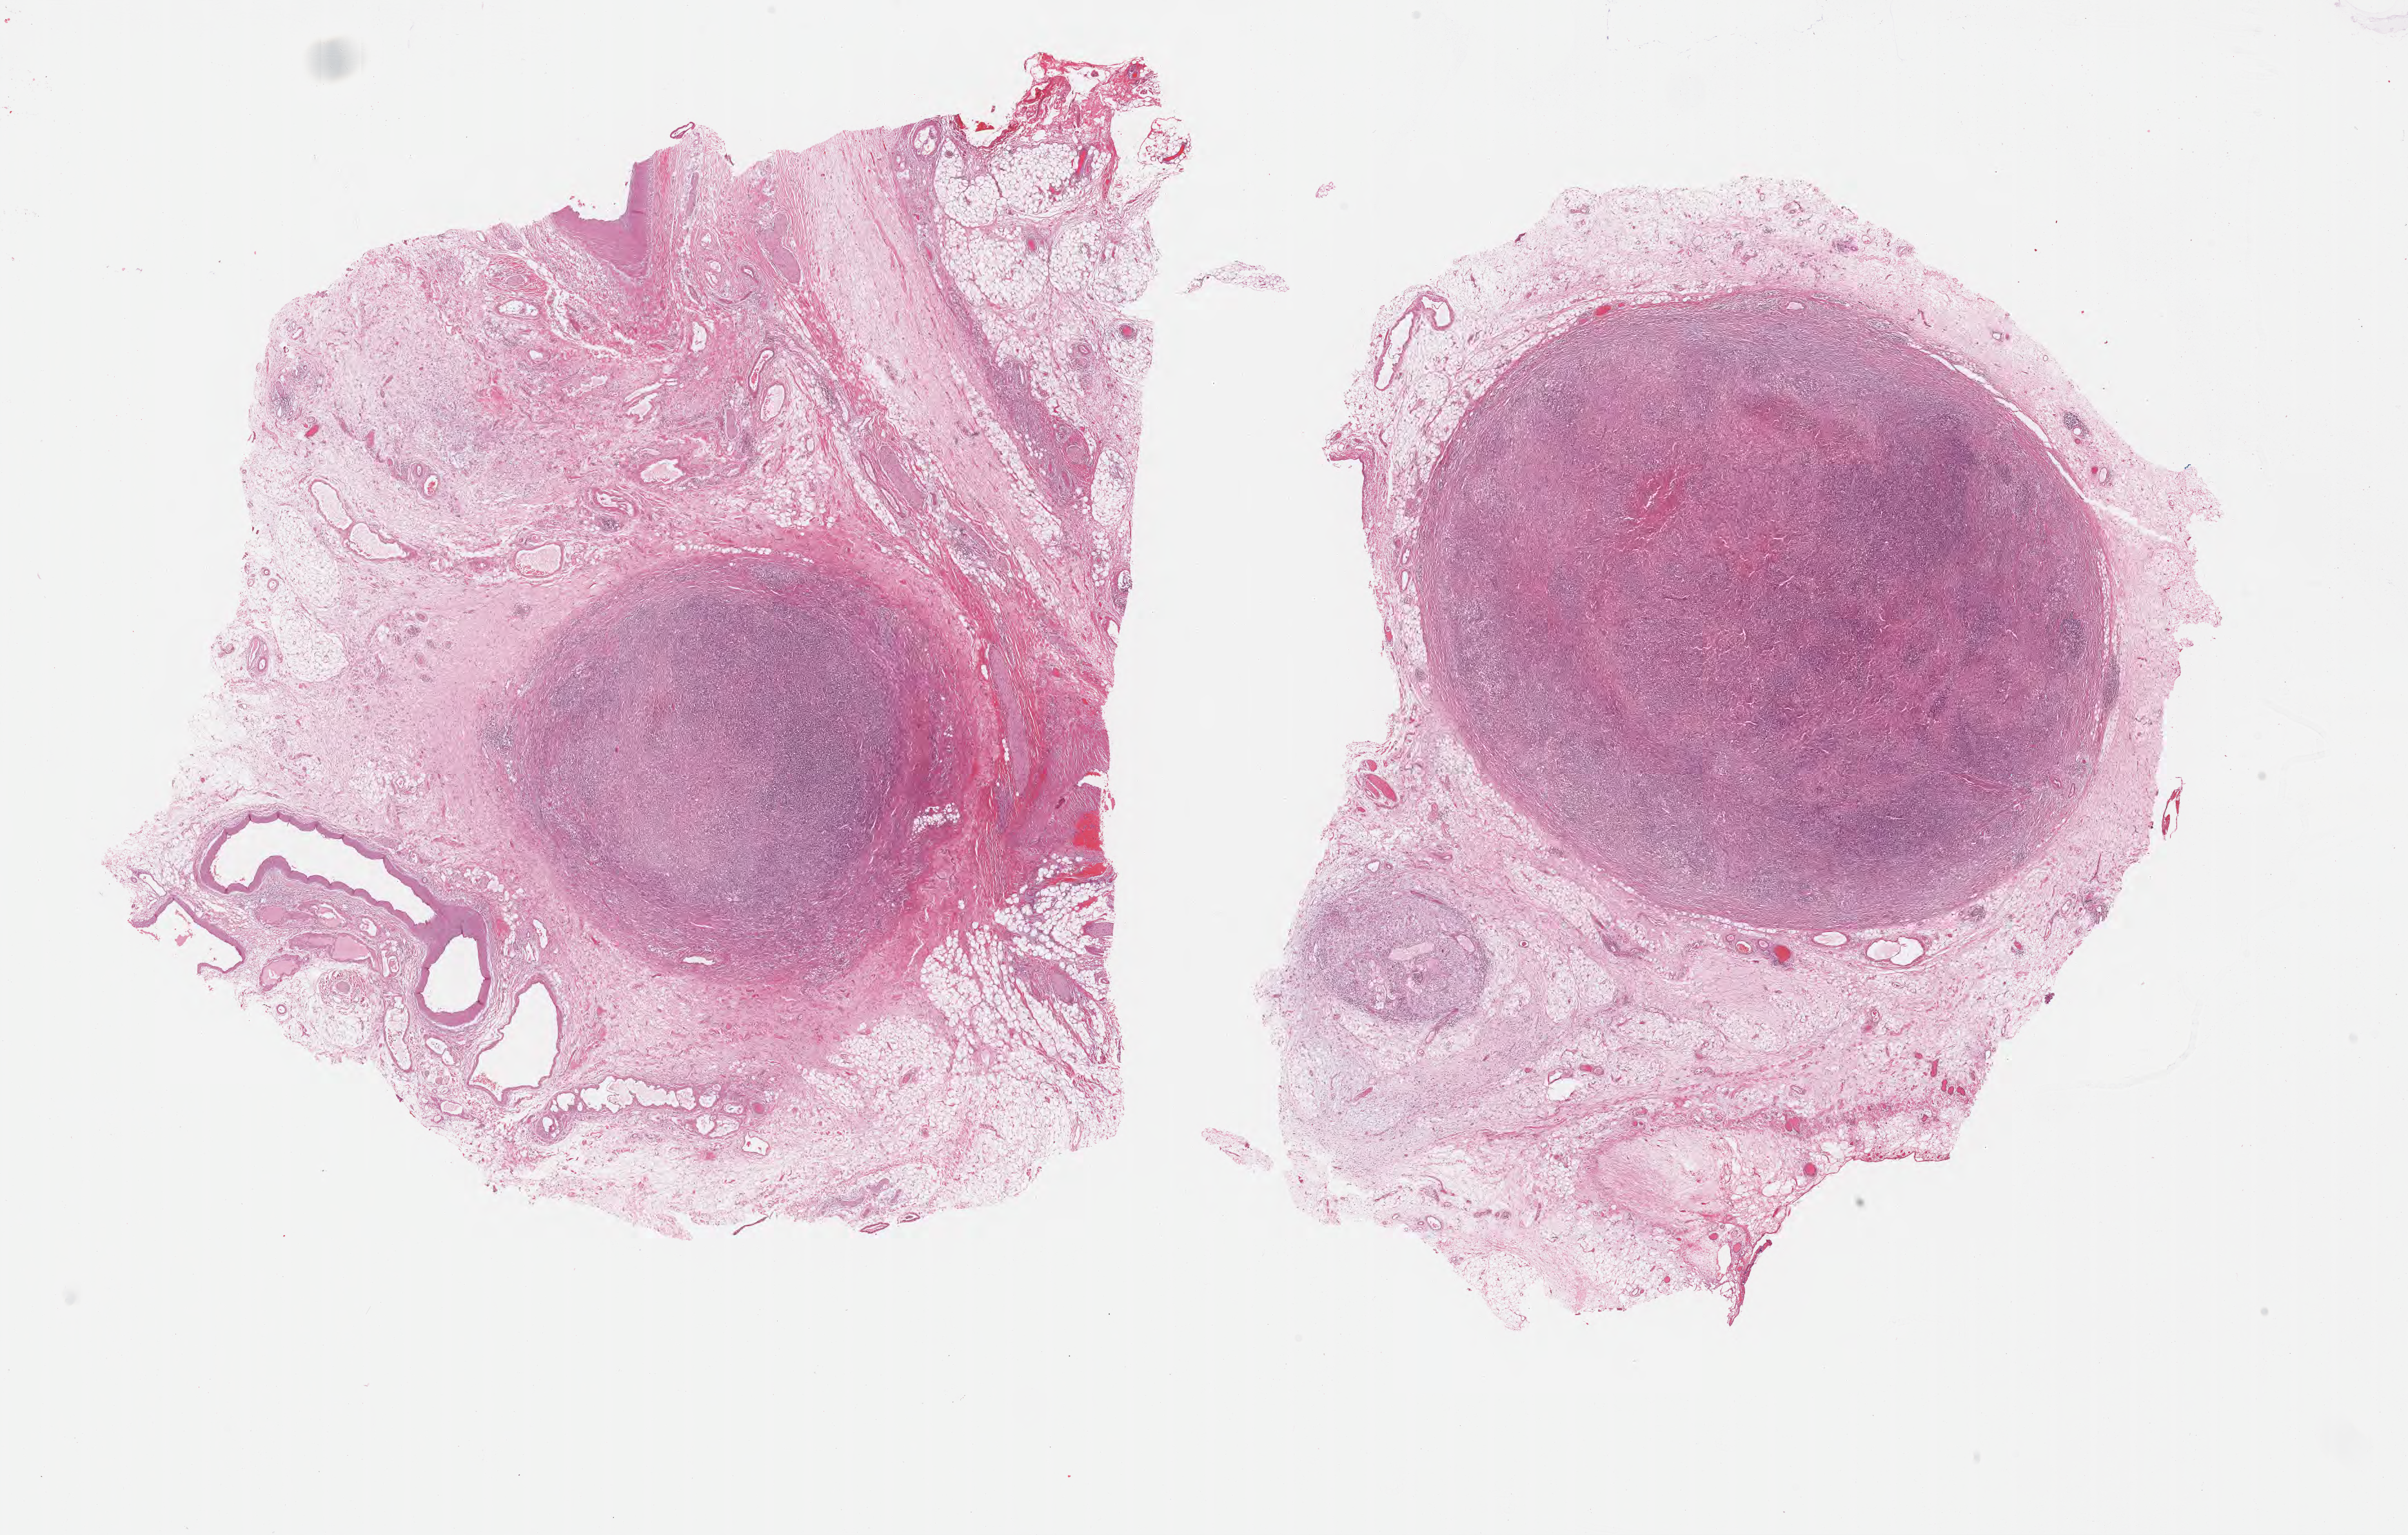
Digitized H&E-stained section, shown as a low-resolution overview of the whole scanned area (about 30.2 x 19.3 mm); formalin-fixed, paraffin-embedded (FFPE) tissue; primary tumor. Patient: female, age 44 years. Composition of this section per pathologist review: tumor cells 60%, tumor nuclei 70%, stromal cells 10%, necrosis 10%, normal cells 20%. Inflammatory infiltration, as recorded: lymphocyte infiltration 70%, monocyte infiltration 20%, neutrophil infiltration 5%.
Histologic diagnosis: Burkitt lymphoma, NOS. Section: bottom of the tissue portion.